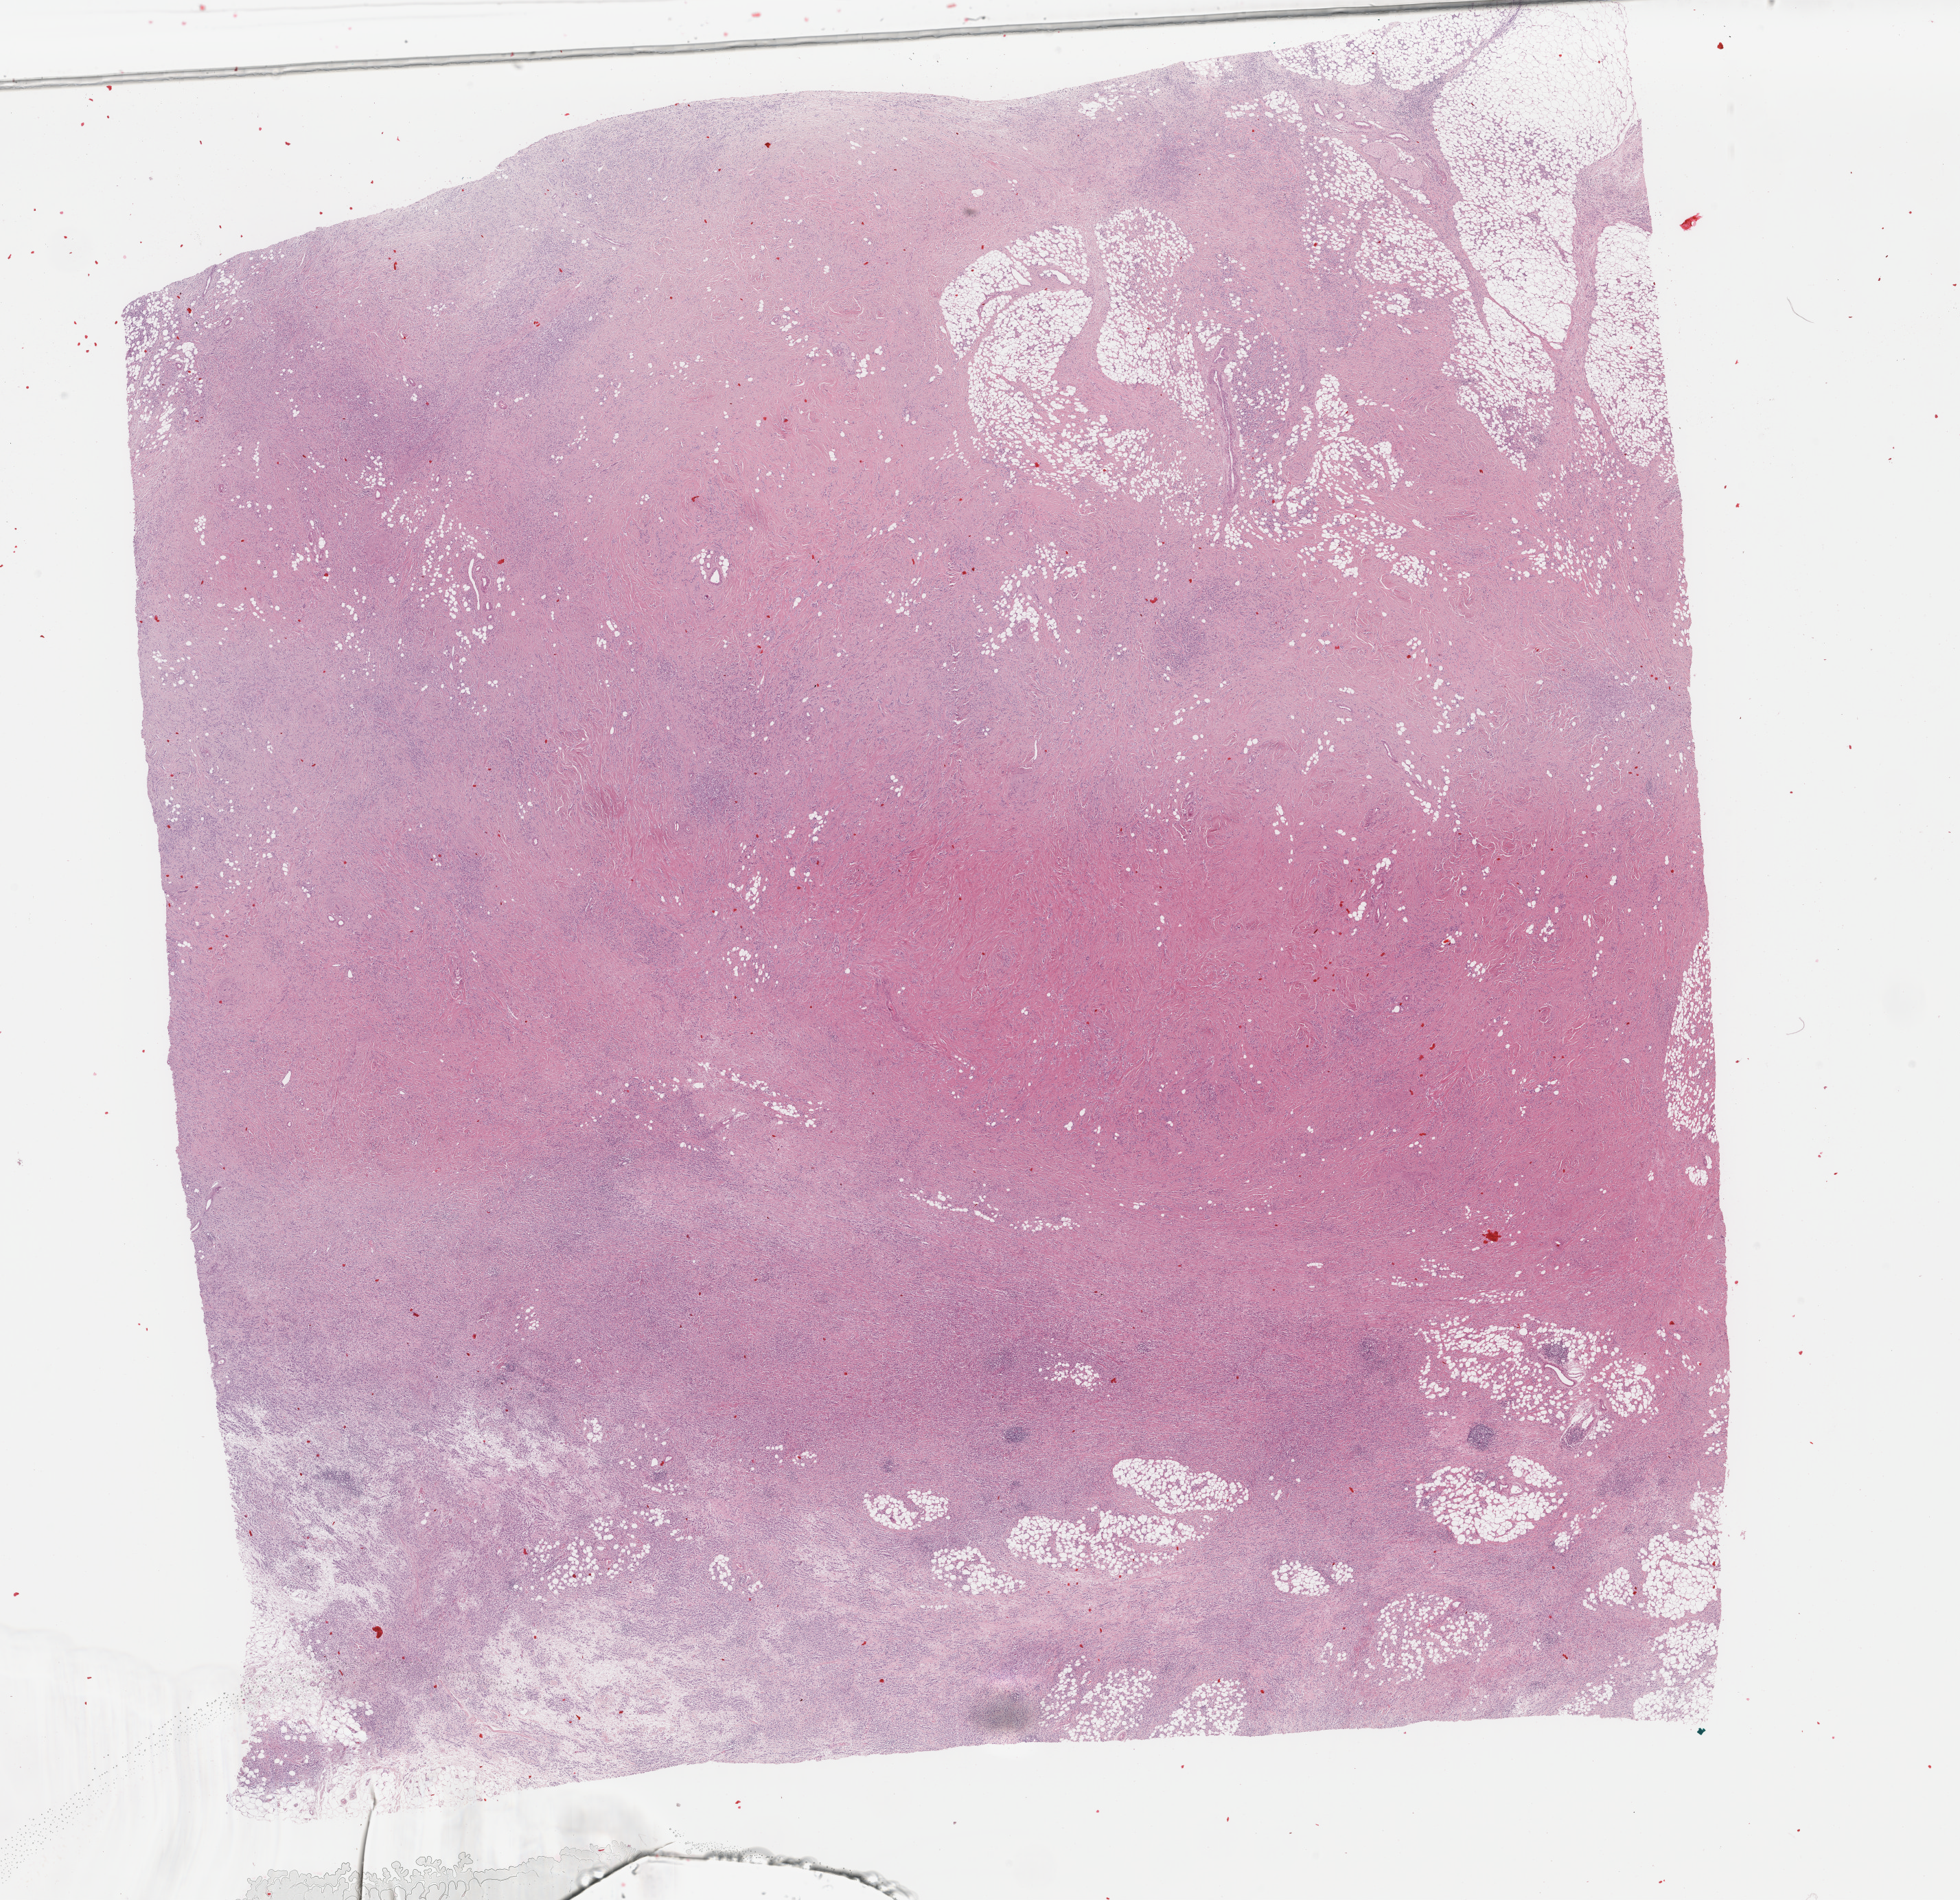
Whole-slide histology image, Hematoxylin and eosin (H&E) stained, whole scanned area (about 22.7 x 22.0 mm) shown as a low-resolution overview. Formalin-fixed paraffin-embedded (FFPE) diagnostic section. Primary tumour sample from the breast. Female, age 80 years at initial diagnosis.
• TNM: T3 N3a MX
• laterality: left
• AJCC pathologic stage: IIIC
• pathologic diagnosis: Lobular carcinoma, NOS